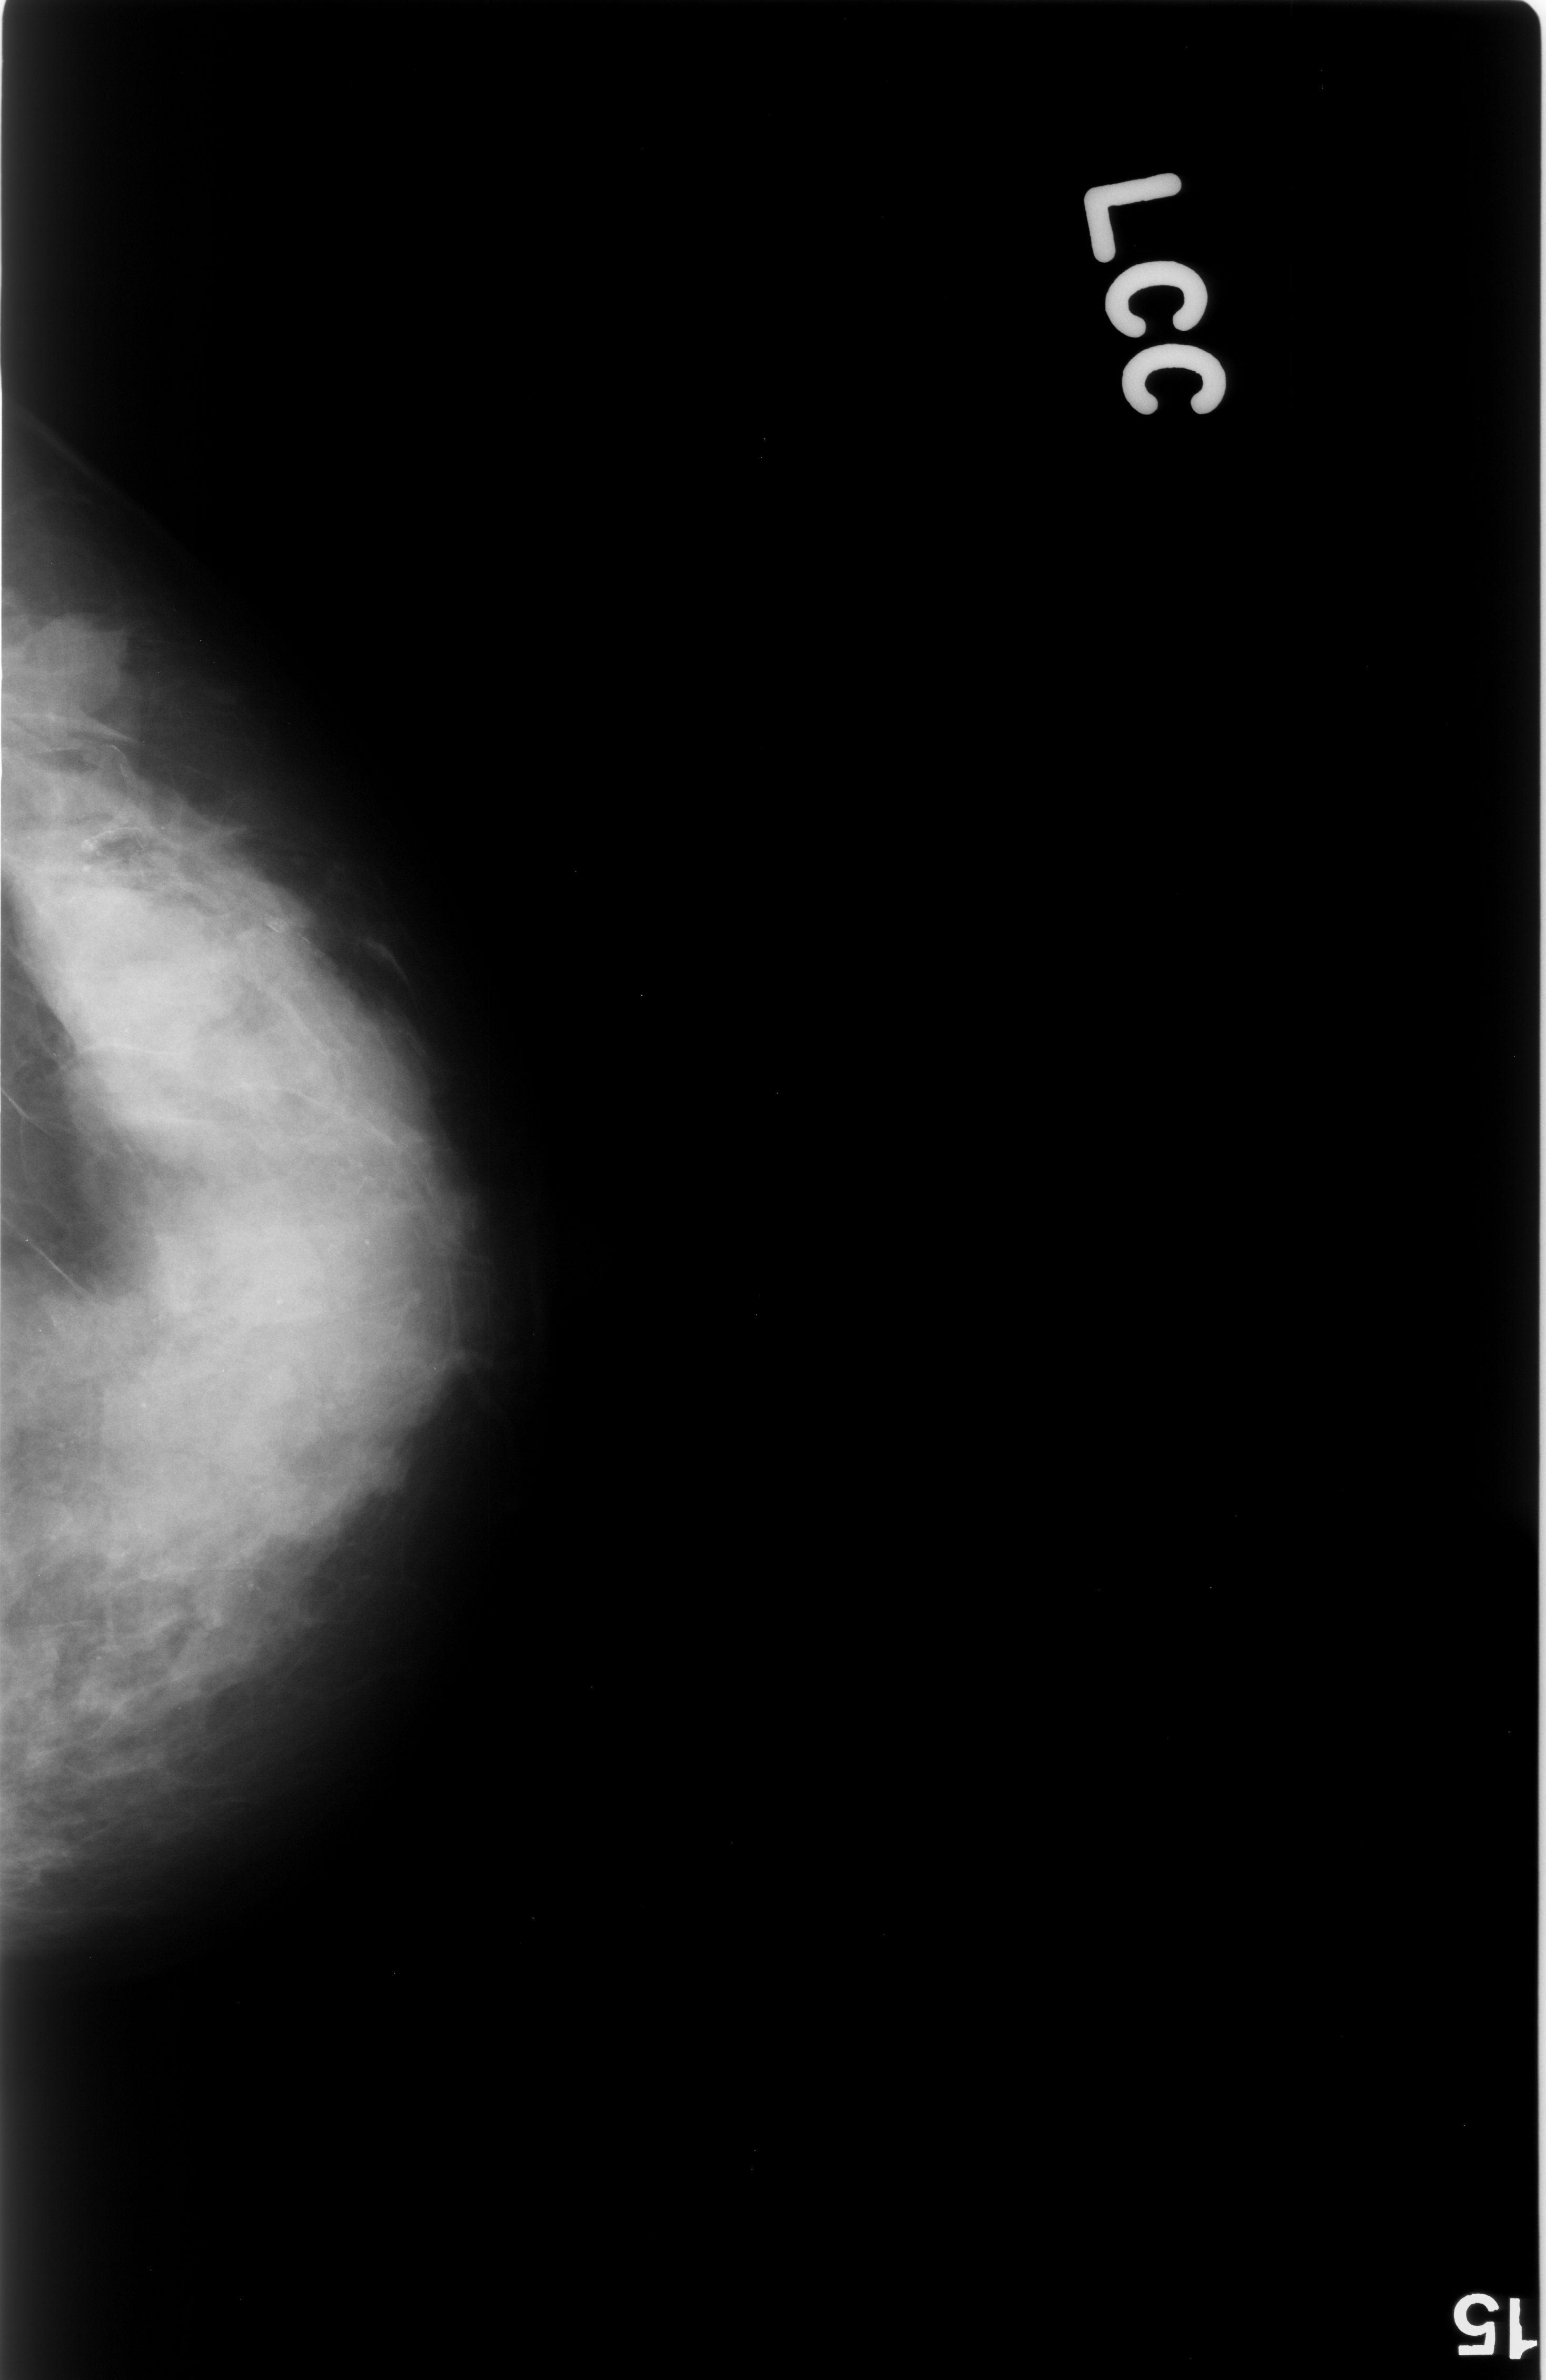
Mammogram (digitized film), left breast, CC view, BI-RADS breast density category 4 (scale 1–4).
Marked findings (only marked abnormalities are described; nothing is implied about the rest of the image): Finding 1 of 2: mass, shape lobulated, margins circumscribed; BI-RADS assessment category 3; subtlety rating 5 on a 1 (subtle) to 5 (obvious) scale; pathology result (as recorded, not read from the image): benign. Finding 2 of 2: mass, shape oval, margins obscured; BI-RADS assessment category 3; subtlety rating 3 on a 1 (subtle) to 5 (obvious) scale; pathology (as recorded): benign.